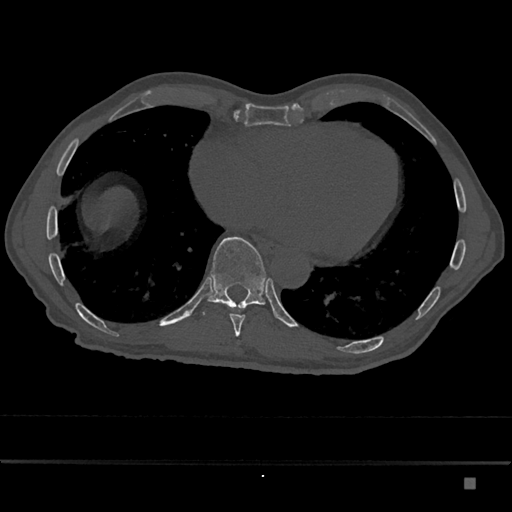
CT including the spine, one axial slice; position 769 of 797 along the scan axis; reconstruction kernel Br40s/3; 120 kVp; bone window (W 1800 / L 400 HU); 0.5 mm slice thickness; 512 × 512 image matrix. Male patient, age 72 years. Case-level facts recorded for this patient, not image findings: primary cancer: prostate.
Annotated regions visible in this slice (semi-automatically segmented with operator editing):
- T10 vertebra: box from (x=202, y=237) to (x=266, y=315) px
- T9 vertebra: (x=230, y=305)–(x=245, y=337)